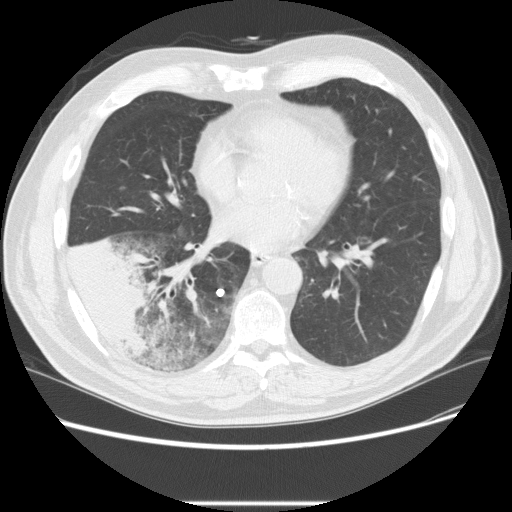
Low-dose screening chest CT, one axial slice; position 98 of 233 along the scan axis; reconstruction kernel STANDARD; 120 kVp; lung window (W 1500 / L -600 HU); 2.5 mm slice thickness; 512 × 512 image matrix.
Annotated regions visible in this slice (outlined manually by an expert reader):
- lesion 3 (tumor, lower lobe of right lung): bounding box [x1, y1, x2, y2] px = [68, 237, 151, 362]